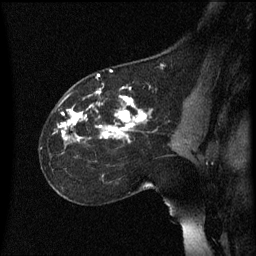
Breast MRI (dynamic contrast-enhanced), one sagittal slice; position 38 of 60 along the scan axis; dynamic contrast-enhanced series, image 2 of 3 at this slice position (ordered by acquisition); 1.5 T; TE 4.2 ms, TR 8.4 ms; 2.2 mm slice thickness; 256 × 256 image matrix, field of view 200 × 200 mm. Female patient, age 35 years. Case-level facts recorded for this patient, not image findings: setting: breast cancer imaged before/during neoadjuvant chemotherapy; receptor status: HER2-positive.
Annotated regions visible in this slice (semi-automatically segmented with operator editing):
- analysis volume of interest (the breast-tissue region the enhancement analysis was run in; not a lesion): bounding box [x1, y1, x2, y2] px = [40, 72, 178, 173]
- tumour enhancement mask (voxels above the 70 % enhancement threshold inside the analysis volume of interest): [59, 76, 151, 141]